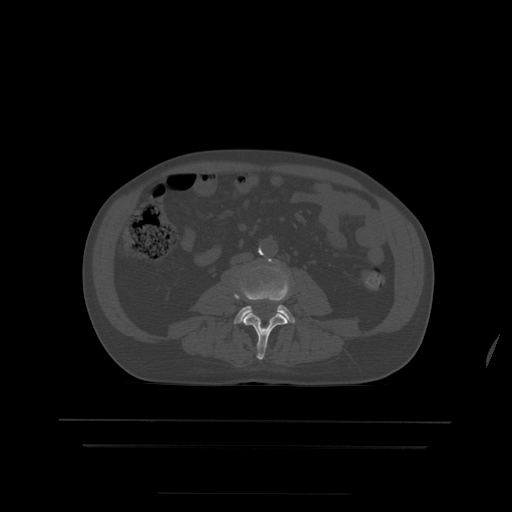
CT including the spine, one axial slice. Position 109 of 522 along the scan axis. Bone window (W 1800 / L 400 HU). 1.25 mm slice thickness. 512 × 512 image matrix. Patient age 68 years. Case-level facts recorded for this patient, not image findings: primary cancer: urothelial.
Outlined on this slice (semi-automatically segmented with operator editing):
- L3 vertebra: box from (x=234, y=294) to (x=288, y=360) px
- L4 vertebra: (x=235, y=259)–(x=295, y=324)